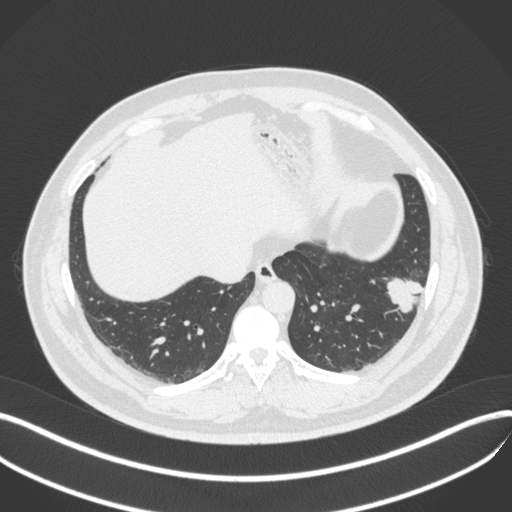
Chest CT, one axial slice; position 118 of 420 along the scan axis; reconstruction kernel B31f; lung window (W 1500 / L -600 HU); 1 mm slice thickness; 512 × 512 image matrix, field of view 400 × 400 mm. Male patient, age 39 years. From the clinical record (not read from this slice): clinical TNM (as recorded): T2a N0 M0; histopathological grade: G2-3.
Outlined on this slice (rectangle marked by the reading radiologist):
- lung tumour (recorded histology: adenocarcinoma): bounding box (x1, y1, x2, y2) in pixels: (380, 271, 426, 320)